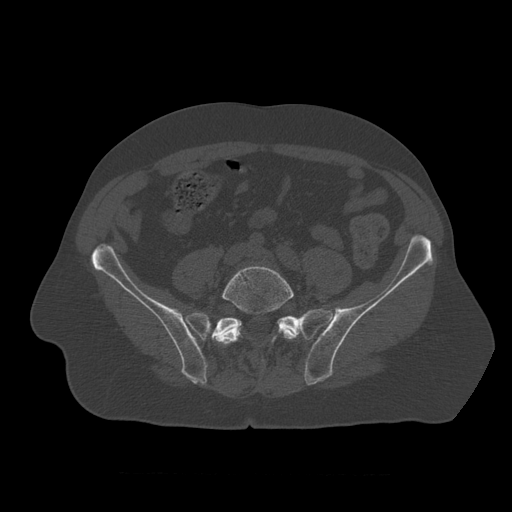
CT including the spine, one axial slice; reconstruction kernel STANDARD; bone window (W 1800 / L 400 HU); 1.25 mm slice thickness; 512 × 512 image matrix. Patient age 75 years. Case-level facts recorded for this patient, not image findings: primary cancer: prostate.
Outlined on this slice (semi-automatic segmentation, software-assisted and operator-edited):
- L5 vertebra: bounding box (x1, y1, x2, y2) in pixels: (216, 265, 298, 363)